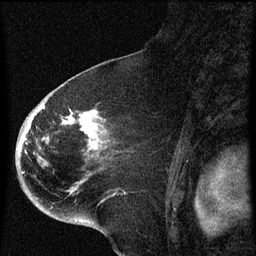
Breast MRI (dynamic contrast-enhanced), one sagittal slice; position 40 of 60 along the scan axis; dynamic contrast-enhanced series, image 2 of 4 at this slice position (ordered by acquisition); 1.5 T; TE 4.2 ms, TR 8 ms; 2 mm slice thickness; 256 × 256 image matrix, field of view 180 × 180 mm. Patient: female, 71 years.
Structures marked on this image (semi-automatically segmented with operator editing):
- analysis volume of interest (the breast-tissue region the enhancement analysis was run in; not a lesion): bounding box <32,86,134,205> (left, top, right, bottom; pixels)
- tumour enhancement mask (voxels above the 70 % enhancement threshold inside the analysis volume of interest): <43,106,99,157>